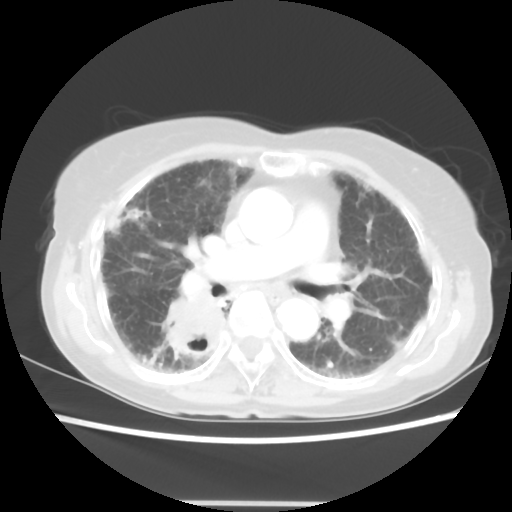
Chest CT, one axial slice. Slice 30 of 52 in the series (ordered by position). Reconstruction kernel STANDARD. 120 kVp. Lung window (W 1500 / L -600 HU). 5 mm slice thickness. 512 × 512 image matrix, field of view 325 × 325 mm. Female patient, age 71 years. Case-level facts recorded for this patient, not image findings: clinical TNM (as recorded): T3 N0 M0.
Structures marked on this image (bounding box drawn by a radiologist):
- lung tumour (recorded histology: squamous cell carcinoma): box from (x=159, y=284) to (x=229, y=379) px